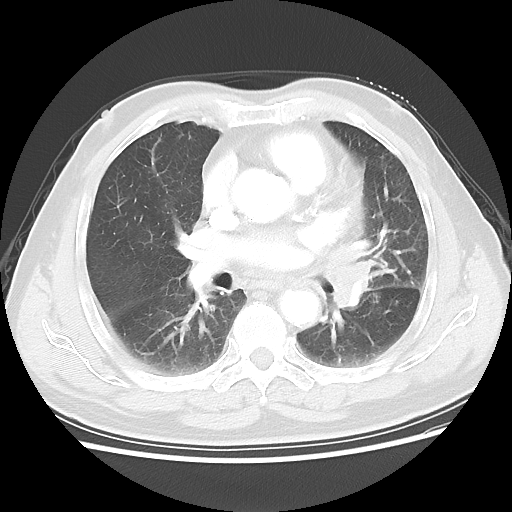
Chest CT, one axial slice. Position 31 of 56 along the scan axis. Lung window (W 1500 / L -600 HU). 5 mm slice thickness. 512 × 512 image matrix. Male patient, age 75 years. Case-level facts recorded for this patient, not image findings: clinical TNM (as recorded): T3 N0 M0.
Structures marked on this image (rectangle marked by the reading radiologist):
- lung tumour (recorded histology: squamous cell carcinoma): bounding box (x1, y1, x2, y2) in pixels: (327, 244, 381, 313)